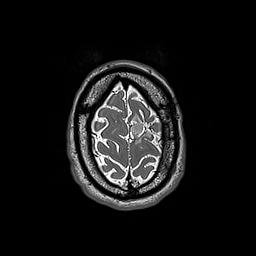
Brain MRI from a brain-tumour surgery series, one axial slice; position 39 of 192 along the scan axis; 1 mm slice thickness; 256 × 256 image matrix, field of view 250 × 250 mm. From the clinical record (not read from this slice): histopathology: Oligodendroglioma; WHO grade: 3; IDH mutation: yes; tumour location: Left Frontal.
Outlined on this slice (expert manual segmentation):
- tumour: bounding box <131,116,146,143> (left, top, right, bottom; pixels)